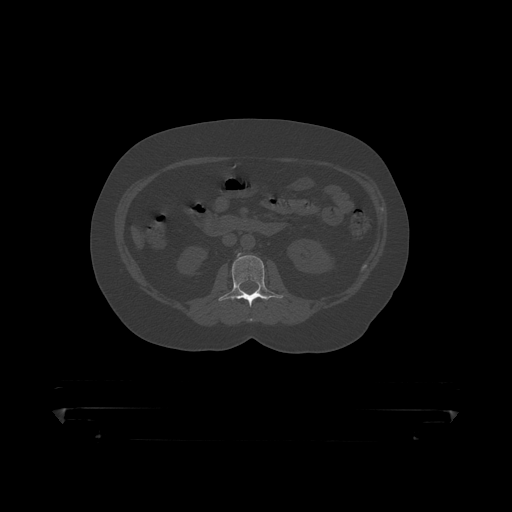
CT including the spine, one axial slice; position 118 of 390 along the scan axis; reconstruction kernel STANDARD; 120 kVp; bone window (W 1800 / L 400 HU); 1.25 mm slice thickness; 512 × 512 image matrix. Patient: male, 60 years. From the clinical record (not read from this slice): primary cancer: prostate.
Outlined on this slice (semi-automatically segmented with operator editing):
- L2 vertebra: box from (x=218, y=254) to (x=283, y=306) px